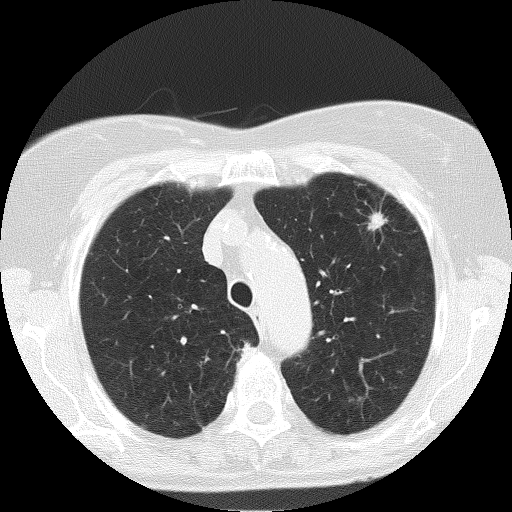
Low-dose screening chest CT, one axial slice; position 132 of 166 along the scan axis; reconstruction kernel FC51; lung window (W 1500 / L -600 HU); 512 × 512 image matrix, field of view 303 × 303 mm.
Outlined on this slice (expert manual segmentation):
- lesion 1 (tumor, upper lobe of left lung): bounding box [x1, y1, x2, y2] px = [370, 213, 384, 230]